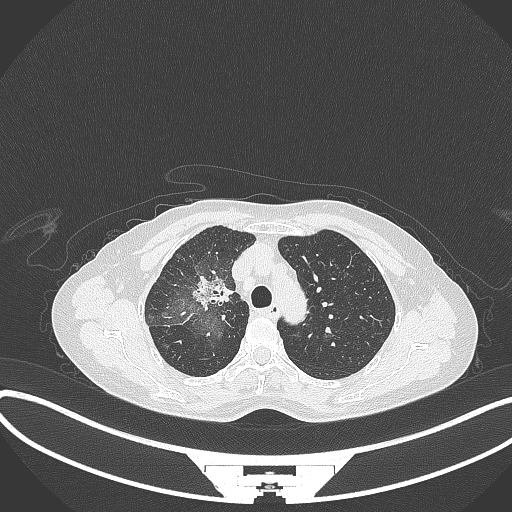
Chest CT, one axial slice; slice 237 of 284 in the series (ordered by position); 120 kVp; lung window (W 1500 / L -600 HU); 1 mm slice thickness; 512 × 512 image matrix, field of view 400 × 400 mm. Female patient, age 59 years. From the clinical record (not read from this slice): clinical TNM (as recorded): T3 N0 M0.
Structures marked on this image (rectangle marked by the reading radiologist):
- lung tumour (recorded histology: adenocarcinoma): box from (x=191, y=271) to (x=233, y=309) px